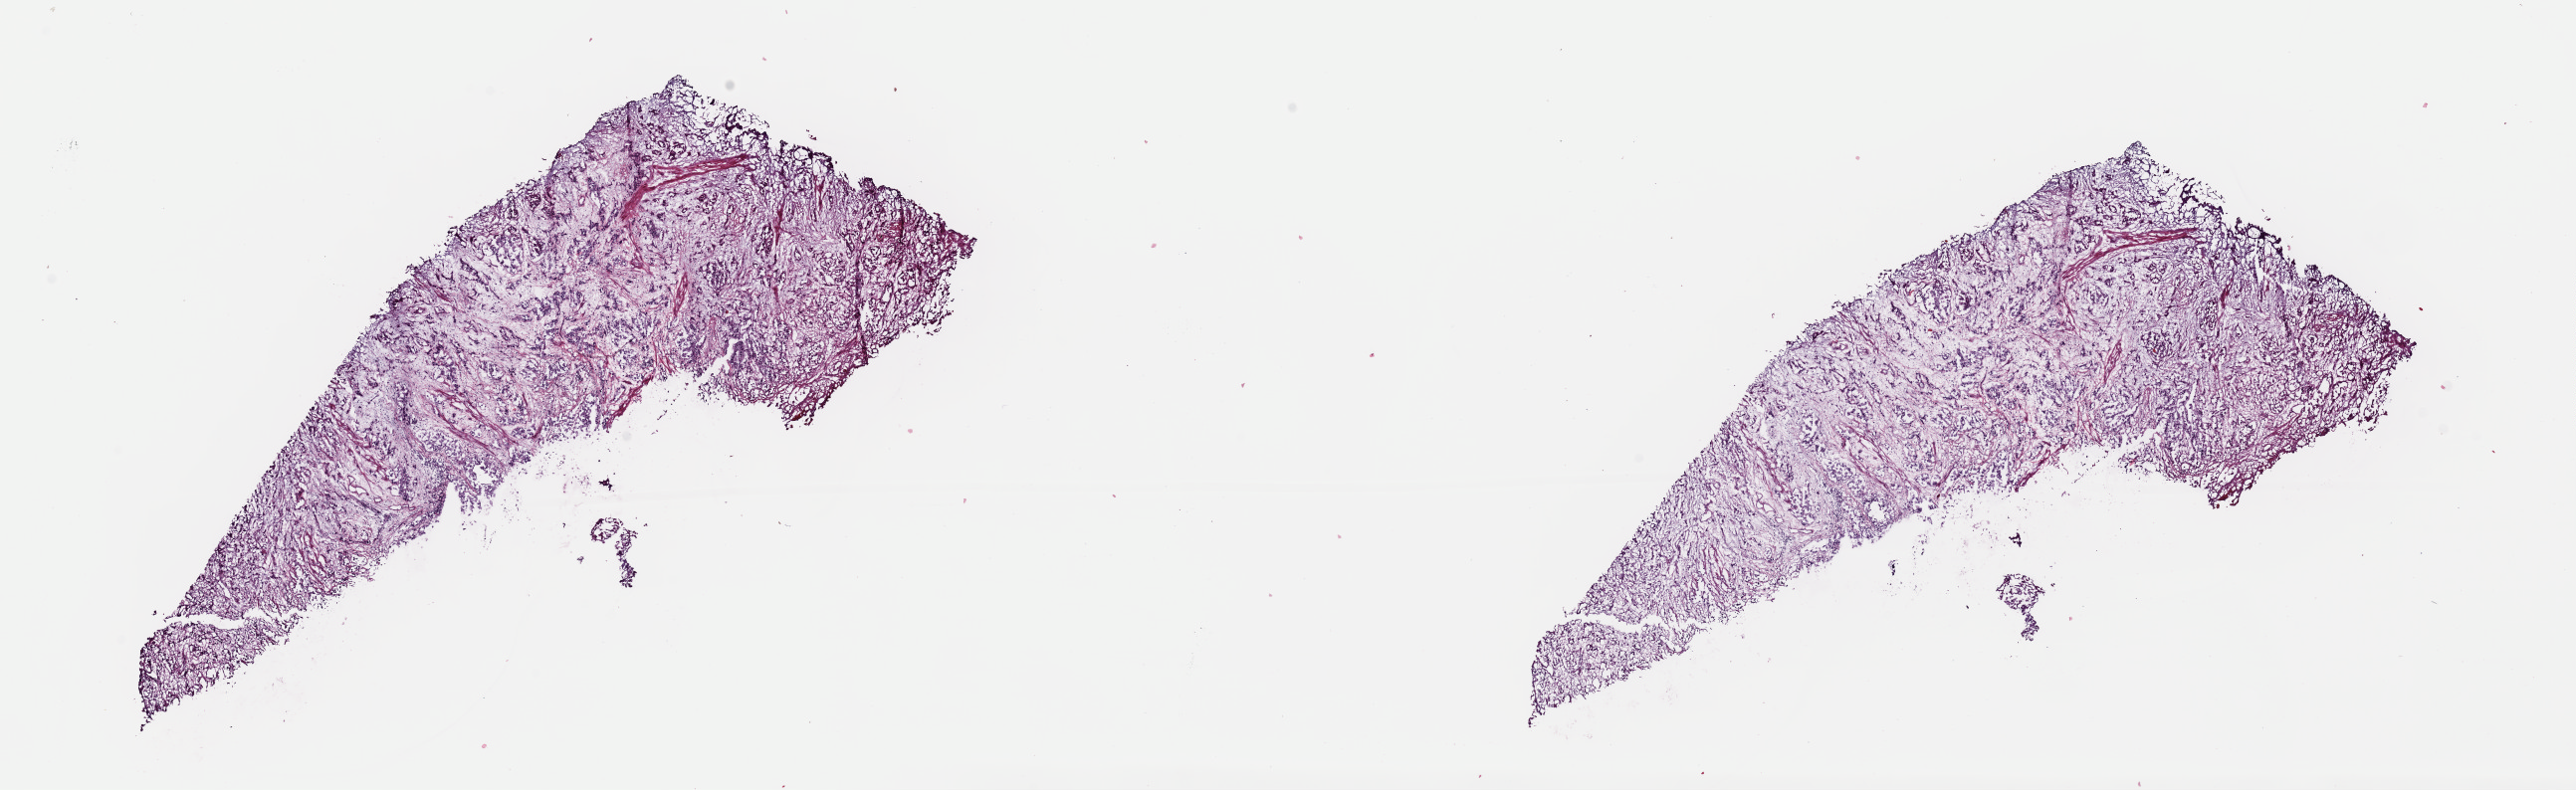
Hematoxylin and eosin (H&E) stained whole-slide image — low-resolution overview of the scanned area, about 20.4 x 6.3 mm (slide scanned at 40x). Frozen section from the top of the tissue portion. Bladder, primary tumour sample. Female, age 58 years at initial diagnosis. Histologic grade: high grade. Pathologist review of this section (percent, as recorded): tumour cells 70%, tumour nuclei 70%, normal cells 0%, stromal cells 30%, necrosis 0%. Inflammatory infiltration, as recorded: lymphocyte infiltration 3%, monocyte infiltration 0%, neutrophil infiltration 0%.
* TNM: N0 M0
* diagnosis: Transitional cell carcinoma
* AJCC pathologic stage: II (2nd edition)